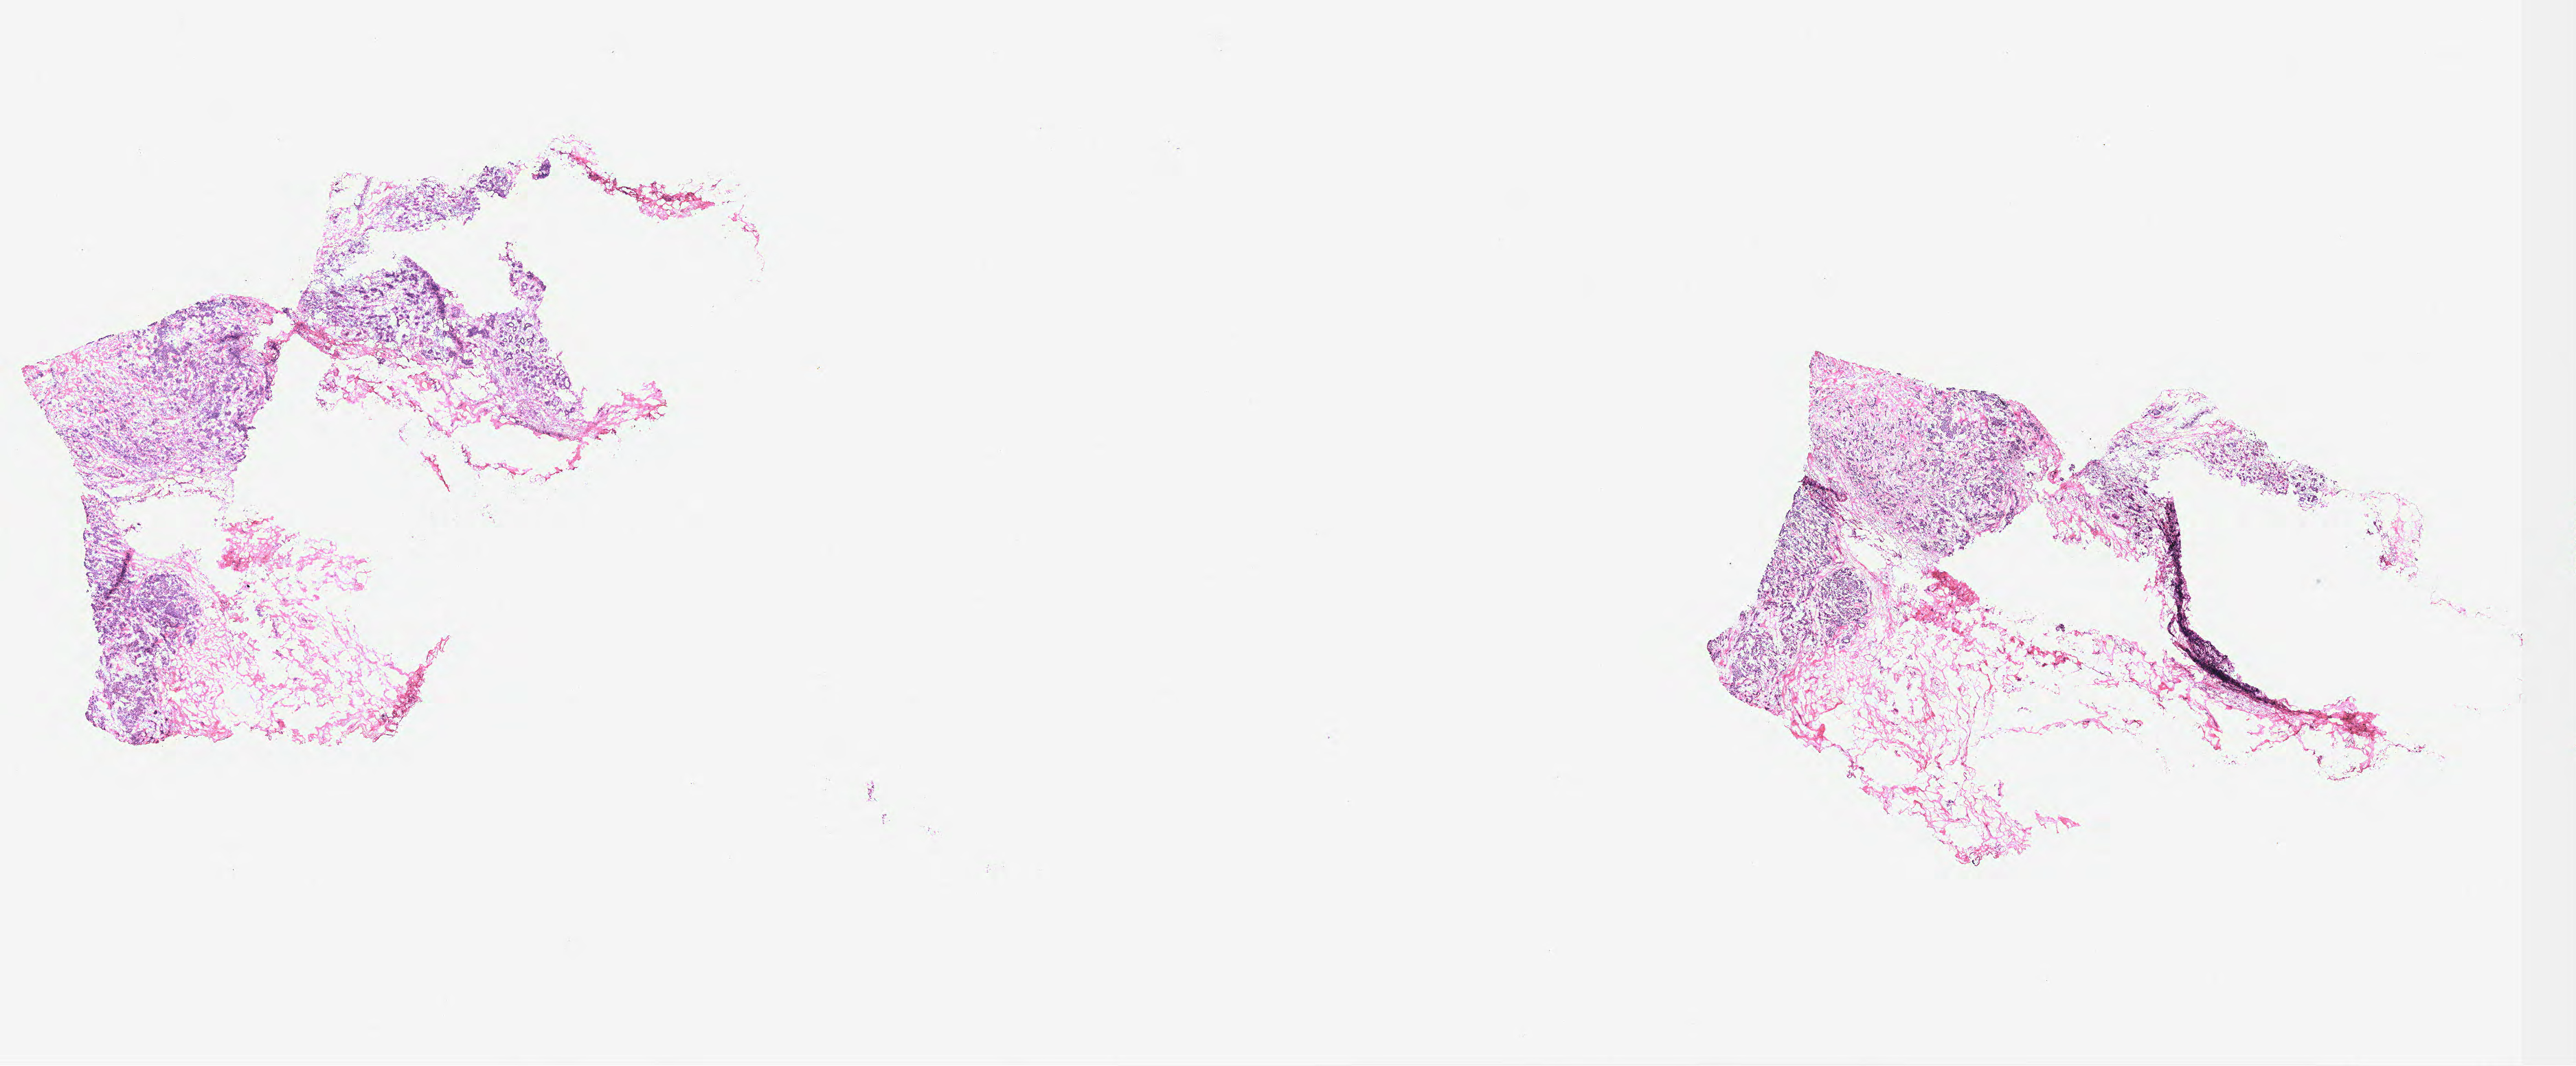
H&E whole-slide image, whole scanned area (about 30.0 x 12.4 mm, from a 40x scan) shown as a low-resolution overview; breast, tissue type not recorded.
* patient diagnosis (cohort enrolment): breast cancer (breast)